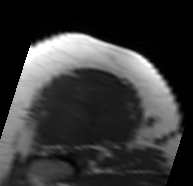
MRI of an extremity soft-tissue mass, one axial slice; position 57 of 91 along the scan axis; MR volume resampled by the dataset authors to the PET/CT grid (not the native acquisition matrix); 3.27 mm slice thickness; 193 × 186 image matrix. Female patient. From the clinical record (not read from this slice): histological type: malignant solitary fibrous tumor; grade: intermediate; site of the primary tumour: right thigh.
Structures marked on this image (expert contour drawn on MRI and transferred to this co-registered scan by the dataset authors):
- gross tumour volume including surrounding oedema: bounding box <33,74,137,148> (left, top, right, bottom; pixels)
- gross tumour volume (mass): <33,78,134,148>